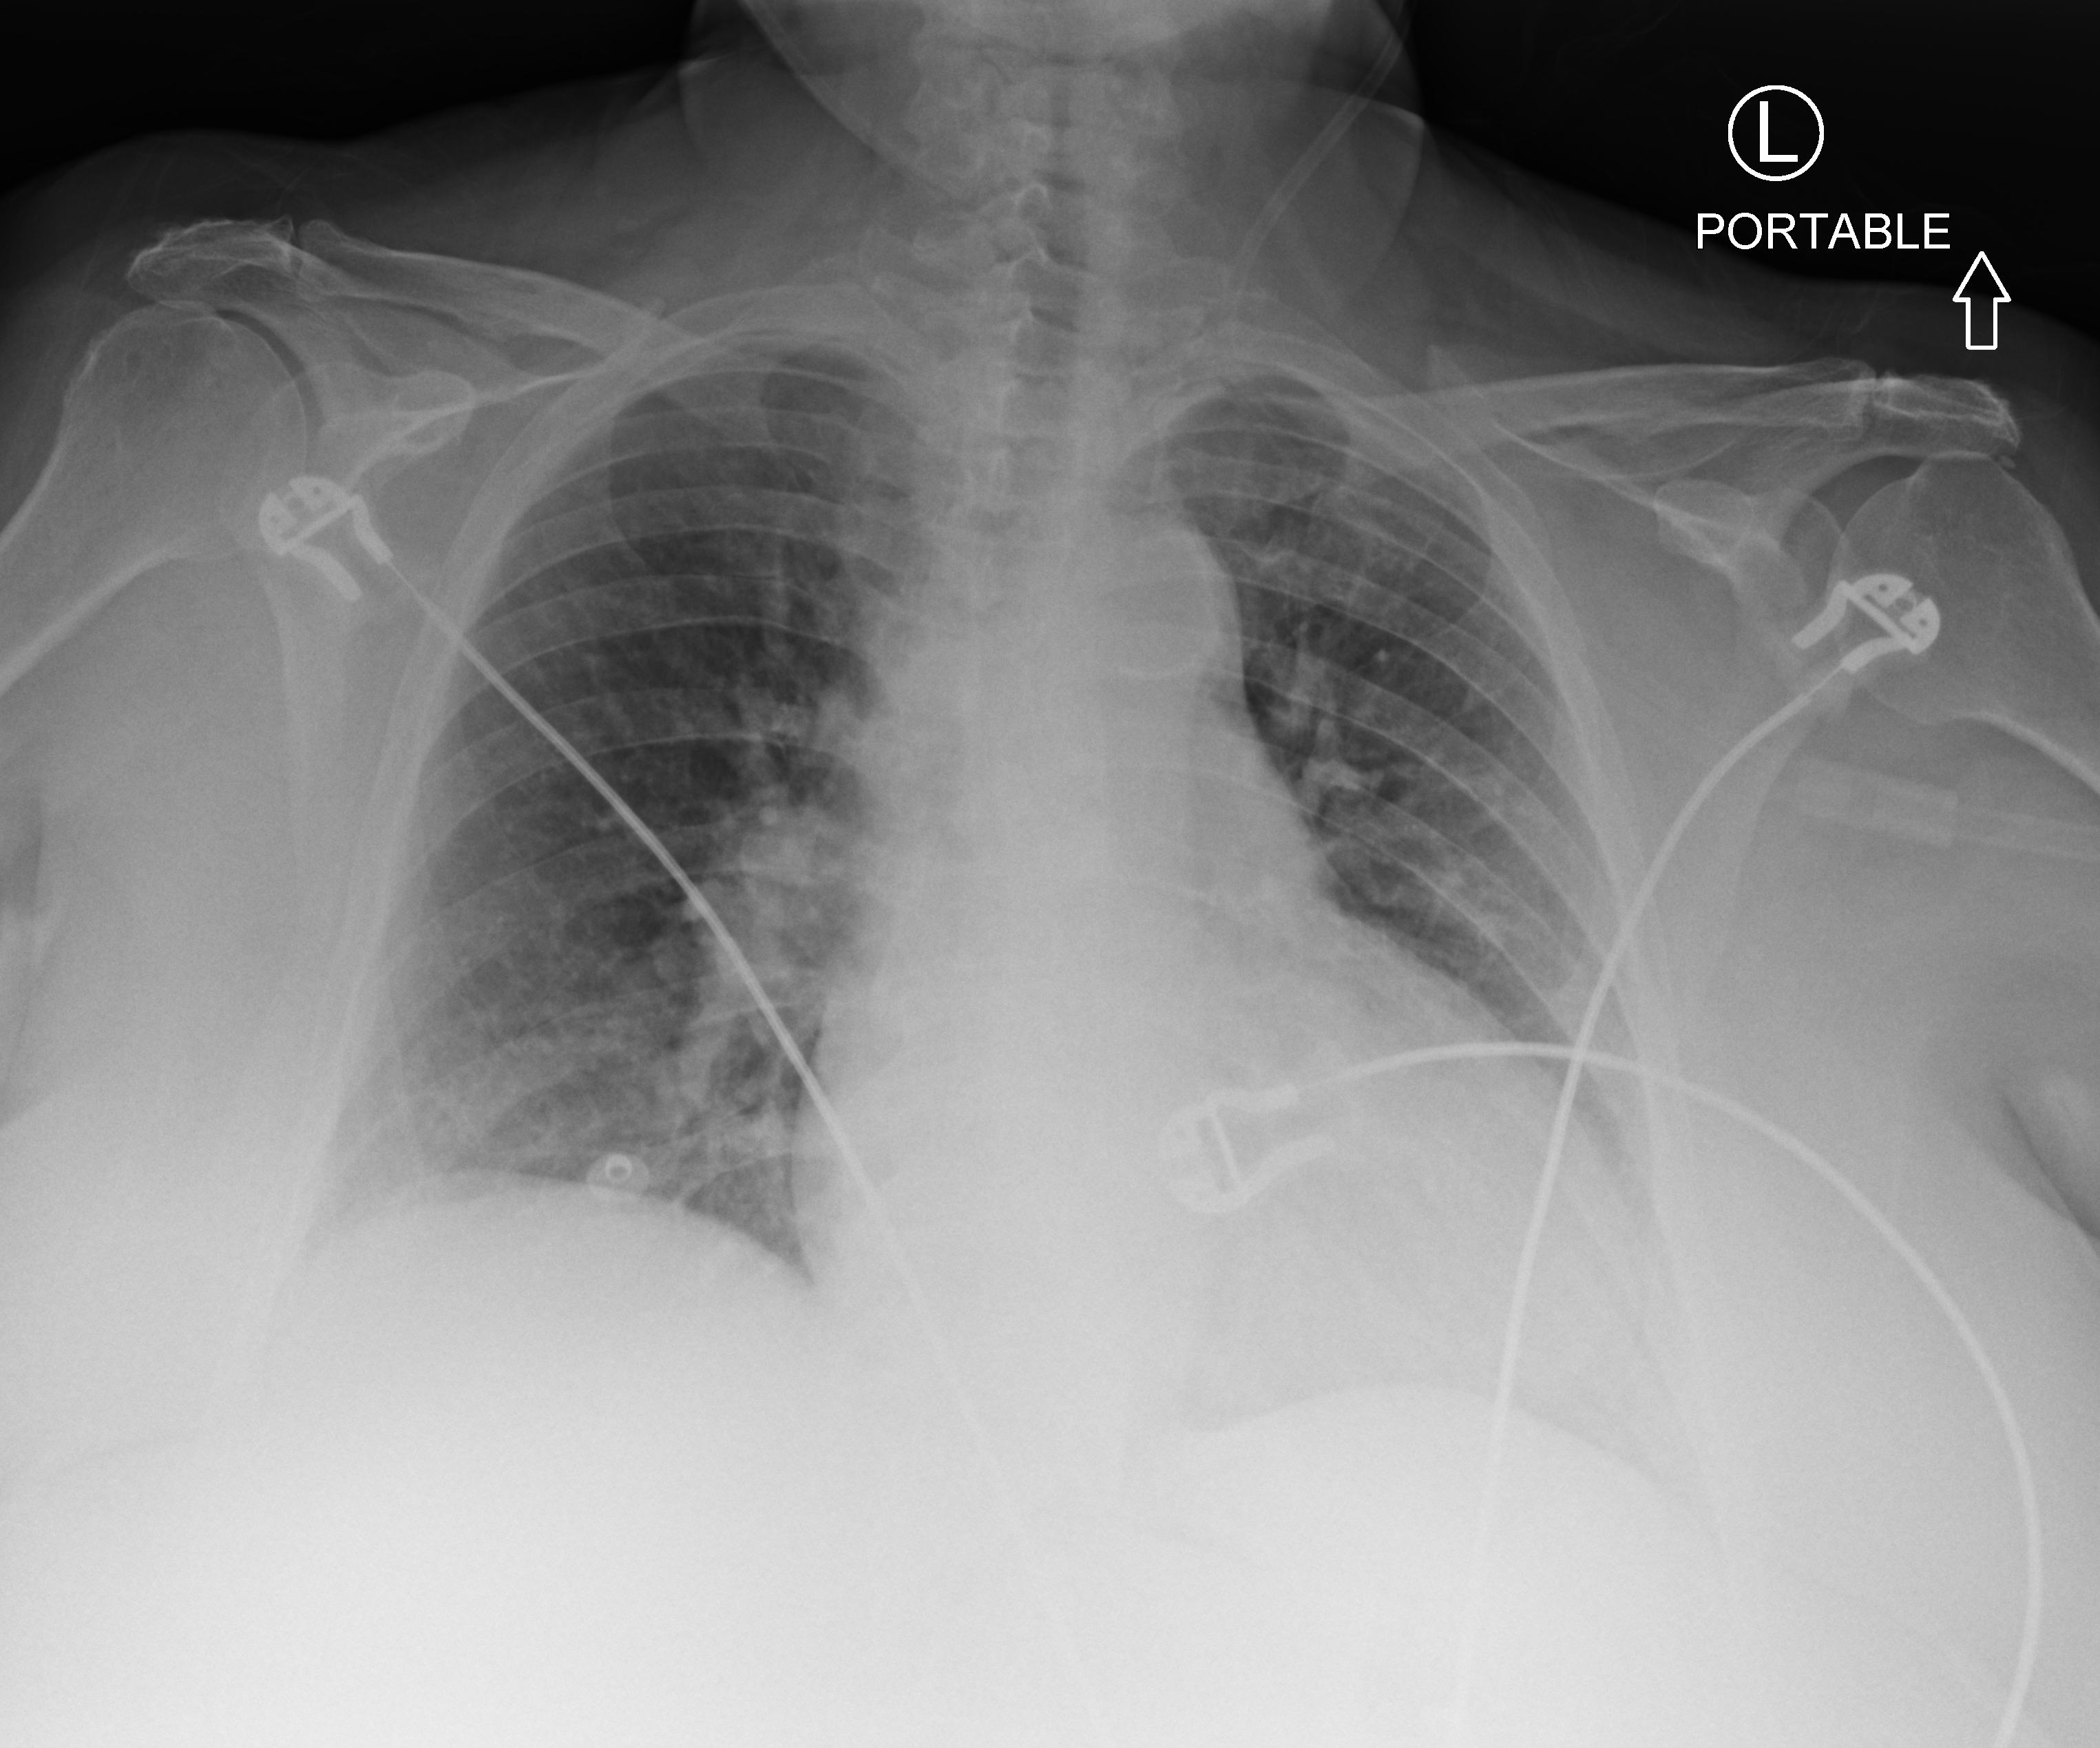
Portable chest radiograph; anteroposterior (AP) projection. Female patient hospitalised with COVID-19, age 75–90 years.
Admission-level facts for this patient (not findings on this image; timing relative to this image not recorded): admitted to intensive care during this hospital stay: no; length of hospital stay: 6 days; diabetes (admission record): no.